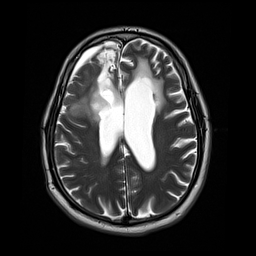
Brain MRI from a brain-tumour surgery series, one axial slice. Slice 16 of 44 in the series (ordered by position). 4 mm slice thickness. 256 × 256 image matrix, field of view 240 × 240 mm. Case-level facts recorded for this patient, not image findings: histopathology: Astrocytoma; WHO grade: 4; IDH mutation: yes.
Annotated regions visible in this slice (manually delineated by an expert):
- tumour: bounding box <72,91,109,124> (left, top, right, bottom; pixels)